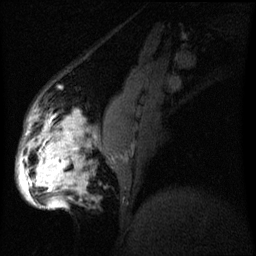
Breast MRI (dynamic contrast-enhanced), one sagittal slice. Slice 19 of 60 in the series (ordered by position). Dynamic contrast-enhanced series, image 2 of 3 at this slice position (ordered by acquisition). 1.5 T. TE 4.2 ms, TR 8 ms. 2.2 mm slice thickness. 256 × 256 image matrix, field of view 200 × 200 mm. Patient: female, 50 years.
Annotated regions visible in this slice (semi-automatic segmentation, software-assisted and operator-edited):
- analysis volume of interest (the breast-tissue region the enhancement analysis was run in; not a lesion): box from (x=19, y=112) to (x=87, y=211) px
- tumour enhancement mask (voxels above the 70 % enhancement threshold inside the analysis volume of interest): (x=20, y=118)–(x=74, y=209)